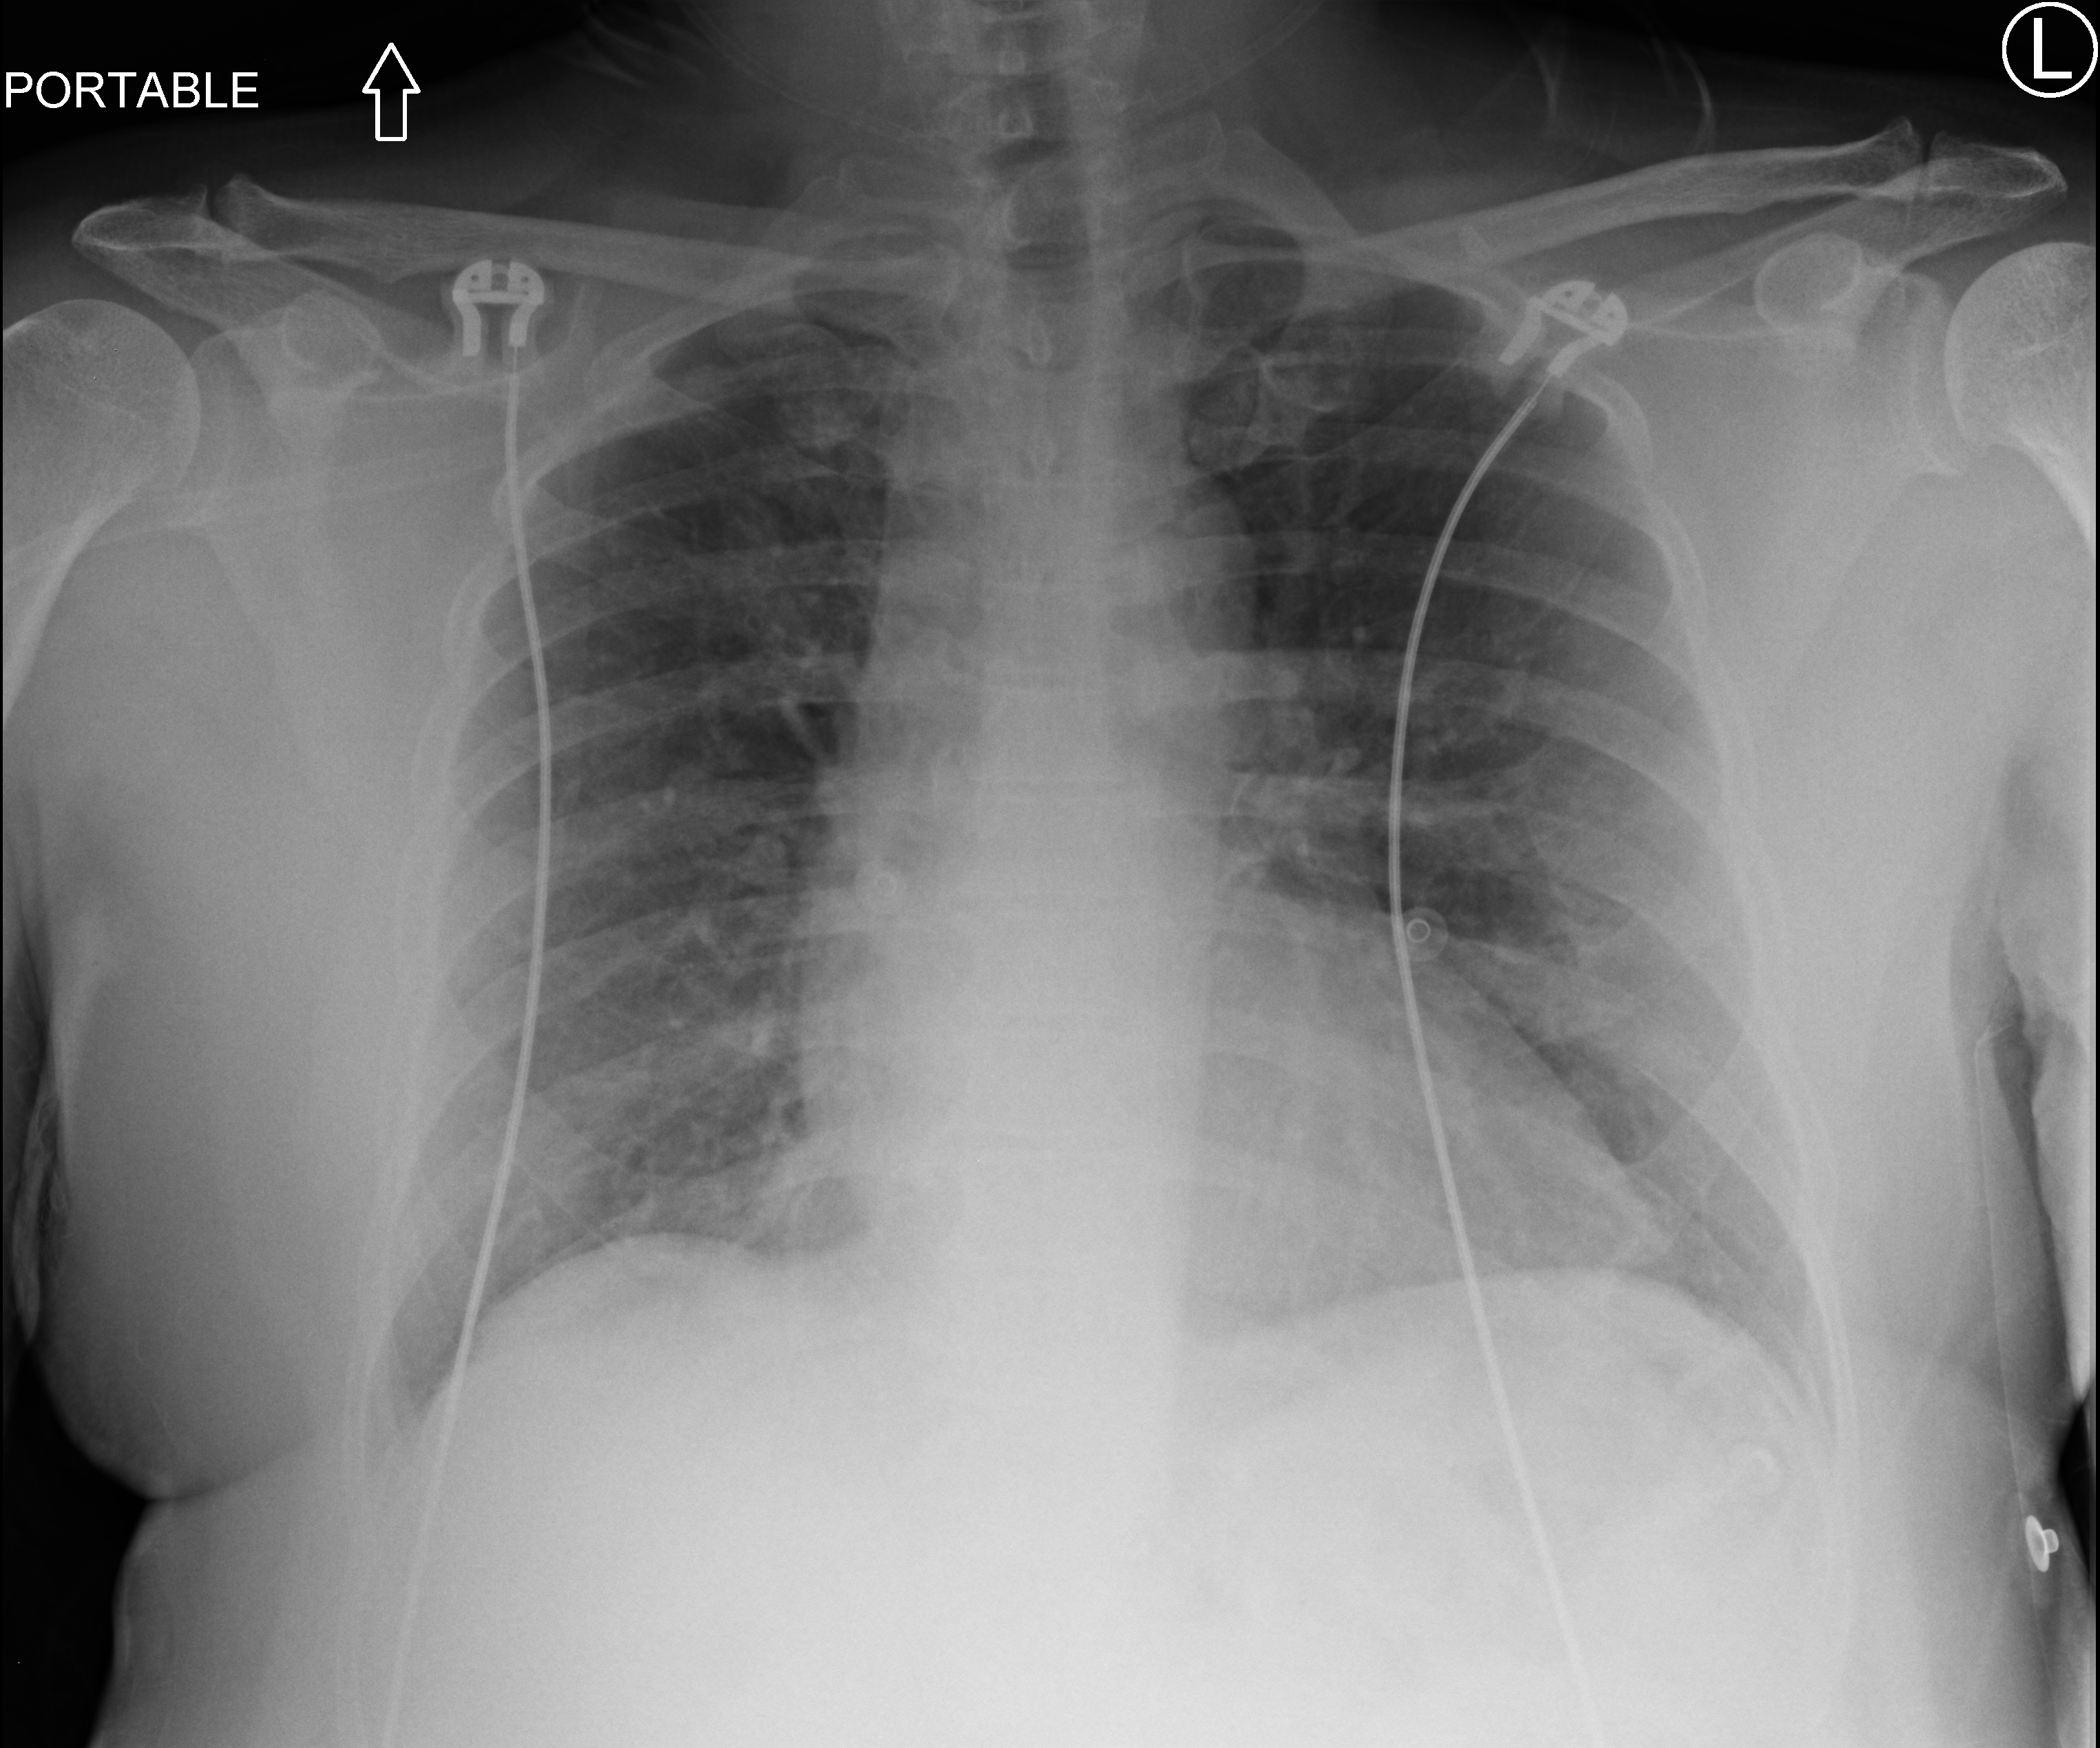
Chest X-ray (portable). Male patient hospitalised with COVID-19, age 18–59 years.
Admission-level facts for this patient (not findings on this image; timing relative to this image not recorded):
- mechanically ventilated during this hospital stay: no